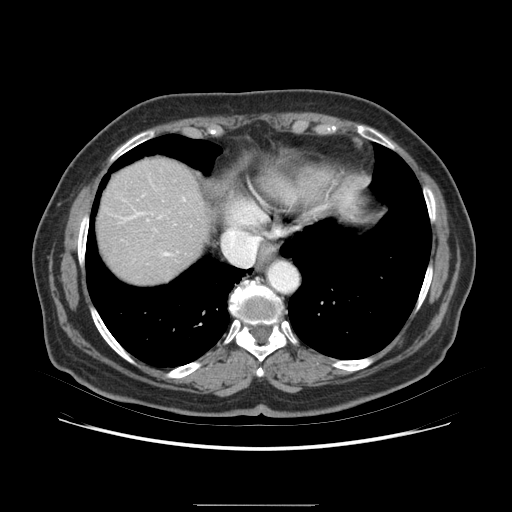
Contrast-enhanced abdominal CT (liver protocol), one axial slice. Position 71 of 79 along the scan axis. 120 kVp. Soft-tissue window (W 400 / L 40 HU). 2.5 mm slice thickness. 512 × 512 image matrix. From the clinical record (not read from this slice): diagnosis: hepatocellular carcinoma (patient treated with transarterial chemoembolisation; whether this scan precedes or follows treatment is not stated here); TNM stage (as recorded): Stage-I; Child-Pugh class: A.
Annotated regions visible in this slice (semi-automatically segmented with operator editing):
- liver parenchyma outside the tumour (the mass and vessels are separate outlines, so this box may not span the whole liver): bounding box <110,166,192,260> (left, top, right, bottom; pixels)